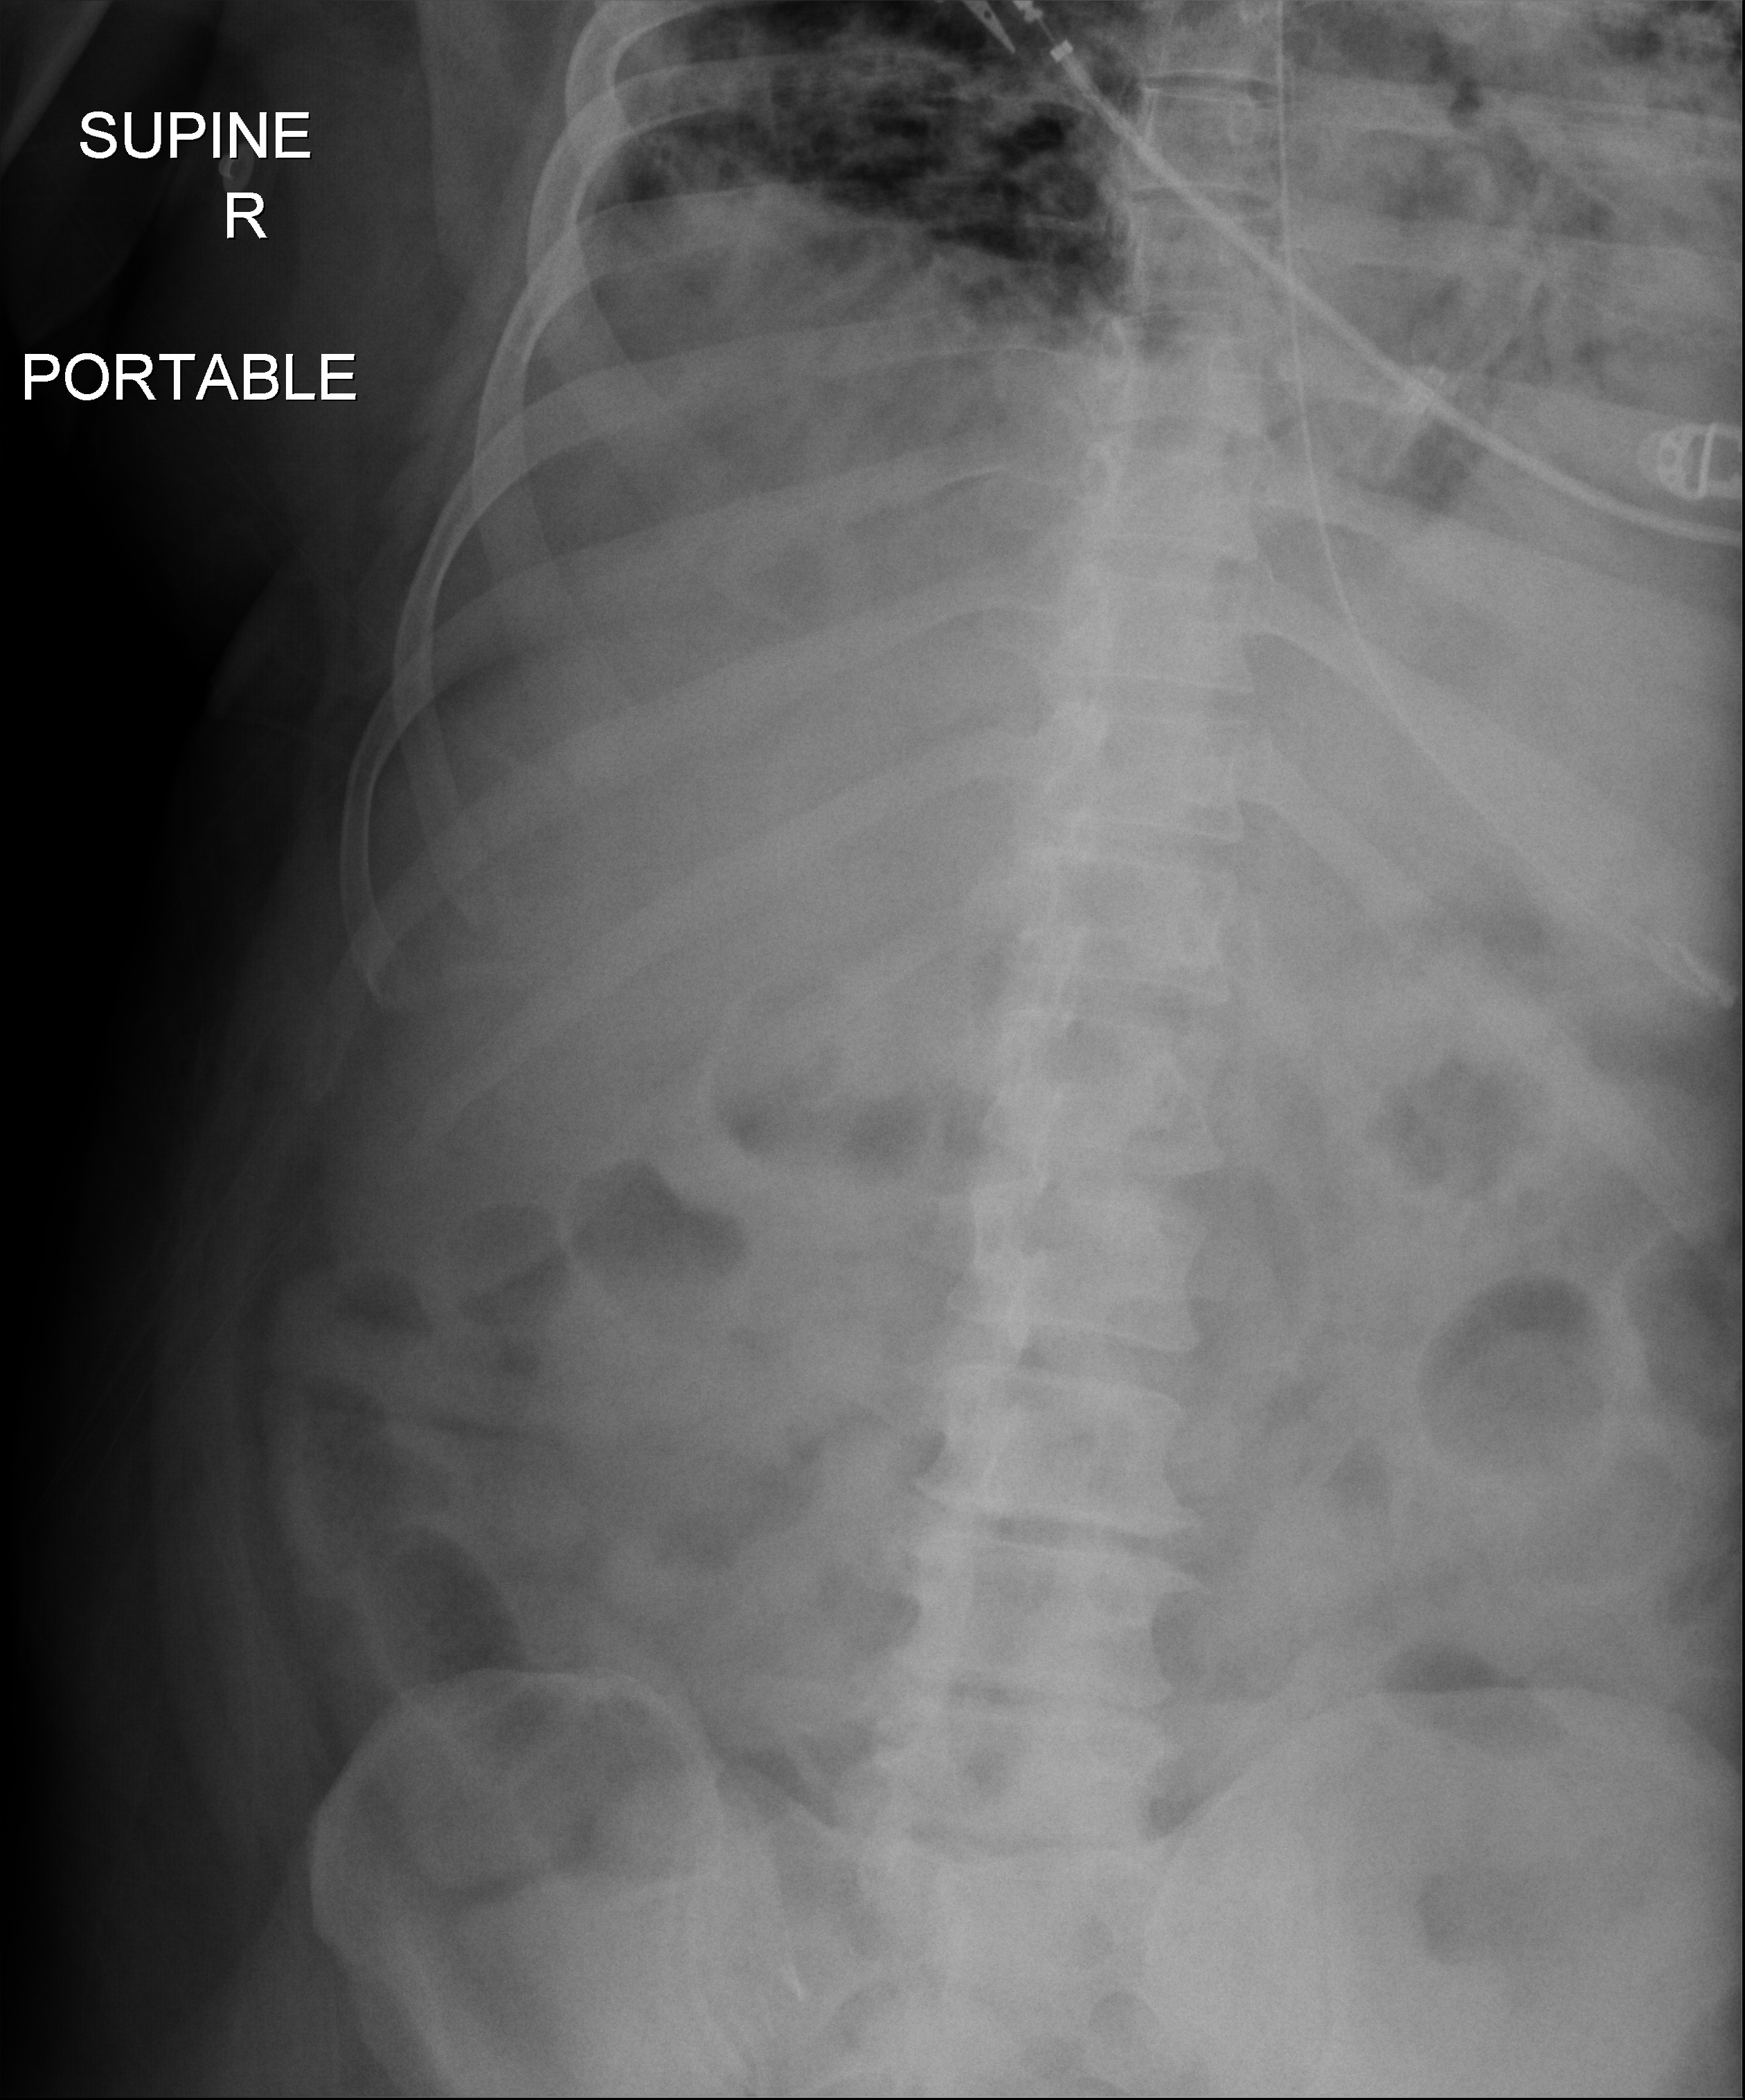
Portable abdomen radiograph. Male patient hospitalised with COVID-19, age 18–59 years.
From the hospital-stay record, not from the radiograph (when in the stay this image was taken is not recorded): admitted to intensive care during this hospital stay: yes.